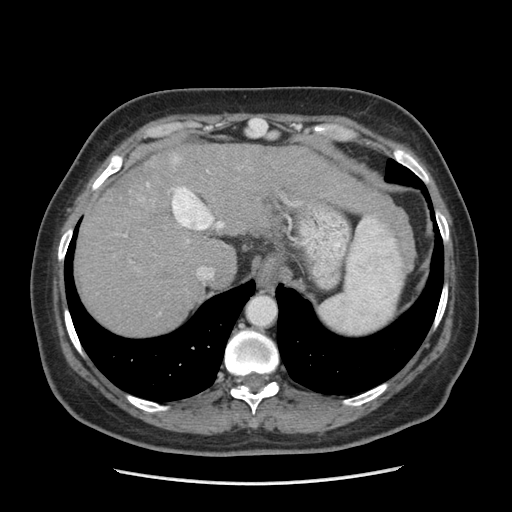
Contrast-enhanced abdominal CT (liver protocol), one axial slice; slice 164 of 185 in the series (ordered by position); 140 kVp; soft-tissue window (W 400 / L 40 HU); 2.5 mm slice thickness; 512 × 512 image matrix. From the clinical record (not read from this slice): diagnosis: hepatocellular carcinoma (patient treated with transarterial chemoembolisation; whether this scan precedes or follows treatment is not stated here); TNM stage (as recorded): Stage-I; Child-Pugh class: A.
Annotated regions visible in this slice (semi-automatic segmentation, software-assisted and operator-edited):
- abdominal aorta: bounding box (x1, y1, x2, y2) in pixels: (247, 297, 275, 325)
- liver parenchyma outside the tumour (the mass and vessels are separate outlines, so this box may not span the whole liver): (74, 144, 376, 336)
- mass: (128, 175, 165, 211)